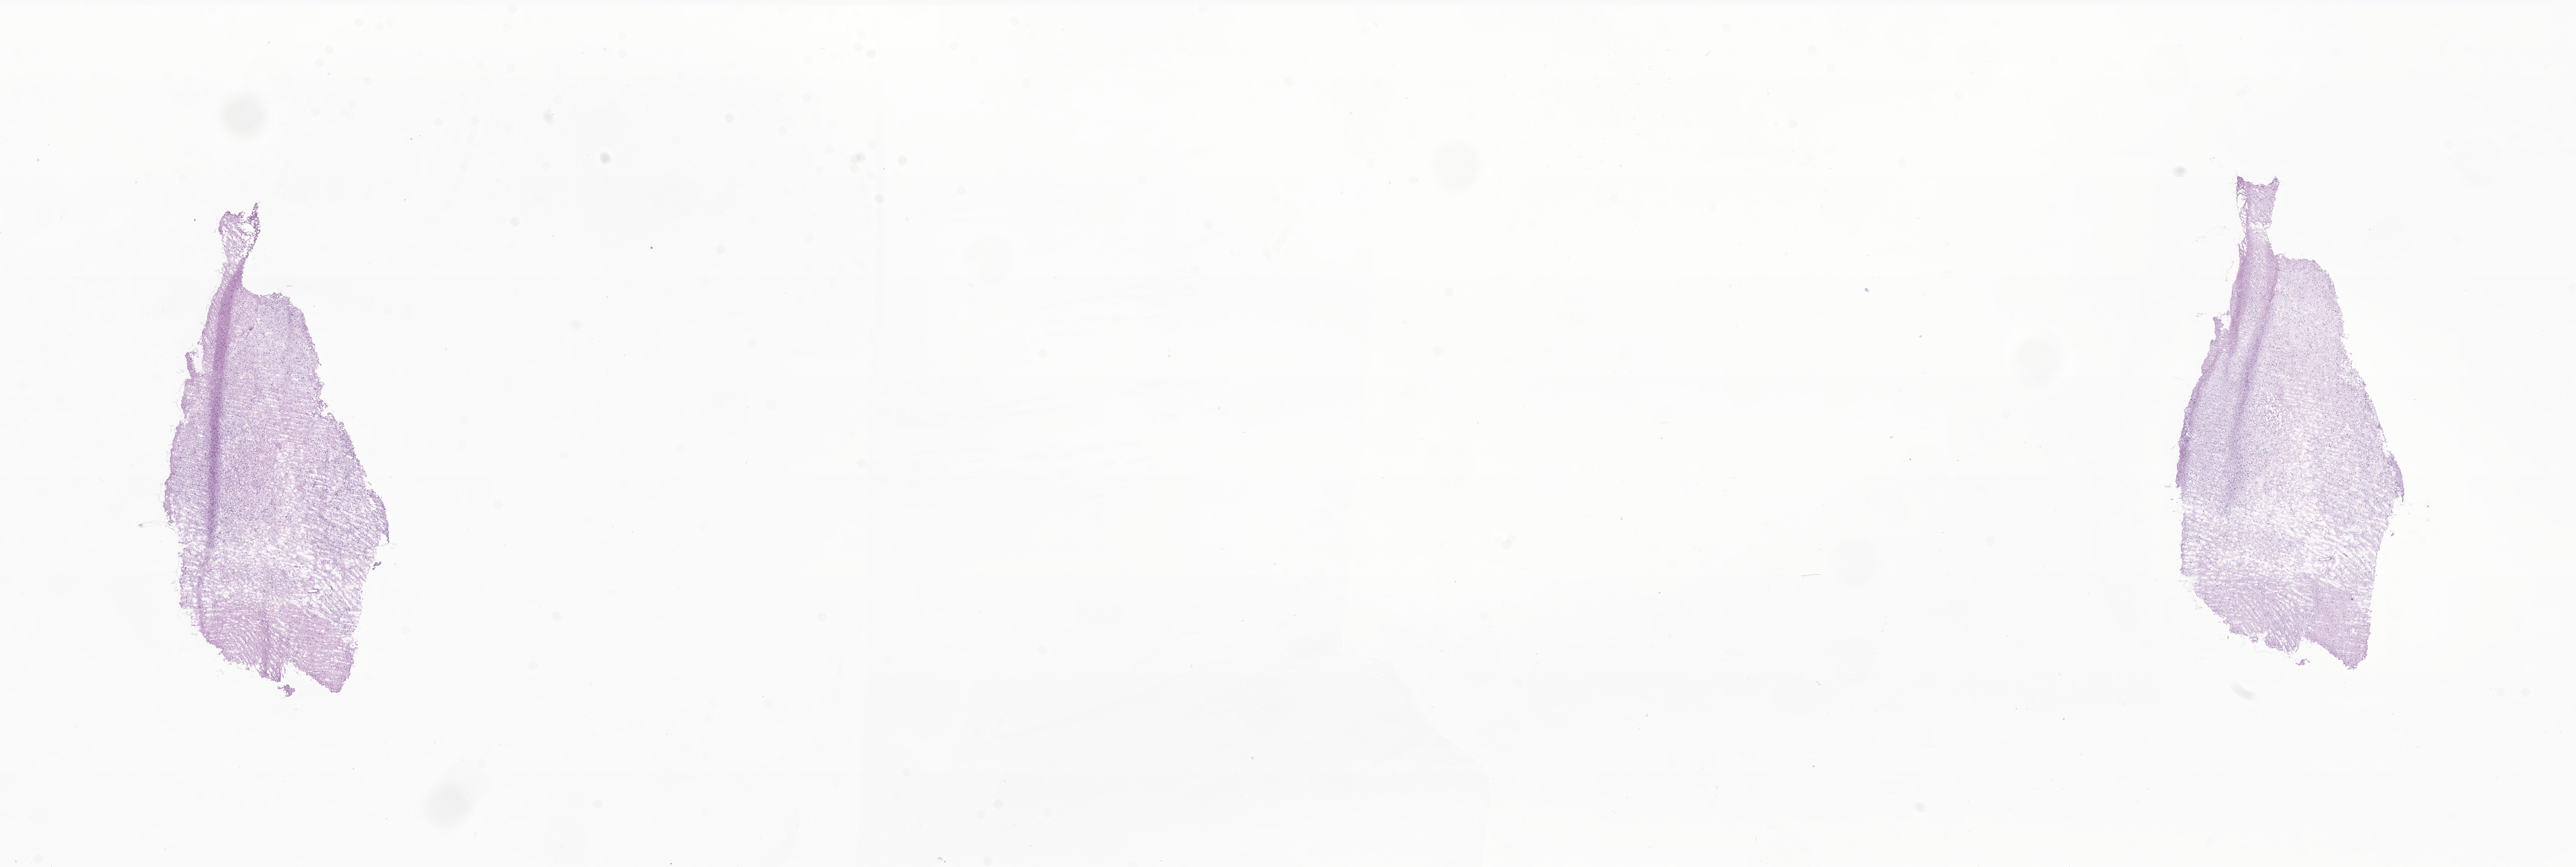
Haematoxylin and eosin whole-slide image of tumor tissue from the brain, shown as a low-resolution overview of the whole scanned area (about 27.7 x 9.3 mm); frozen section (OCT-embedded). Patient female; age 293 months (24 years 5 months).
* diagnosis (ICD-O-3 morphology term): Glioma, malignant